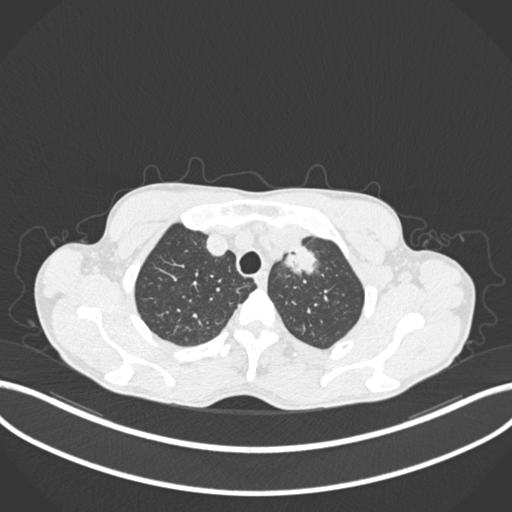
Chest CT, one axial slice; slice 173 of 211 in the series (ordered by position); reconstruction kernel B30f; lung window (W 1500 / L -600 HU); 1 mm slice thickness; 512 × 512 image matrix, field of view 400 × 400 mm. Patient: male, 58 years. Case-level facts recorded for this patient, not image findings: clinical TNM (as recorded): T1c N1 M0.
Structures marked on this image (rectangle marked by the reading radiologist):
- lung tumour (recorded histology: adenocarcinoma): bounding box <276,242,323,281> (left, top, right, bottom; pixels)